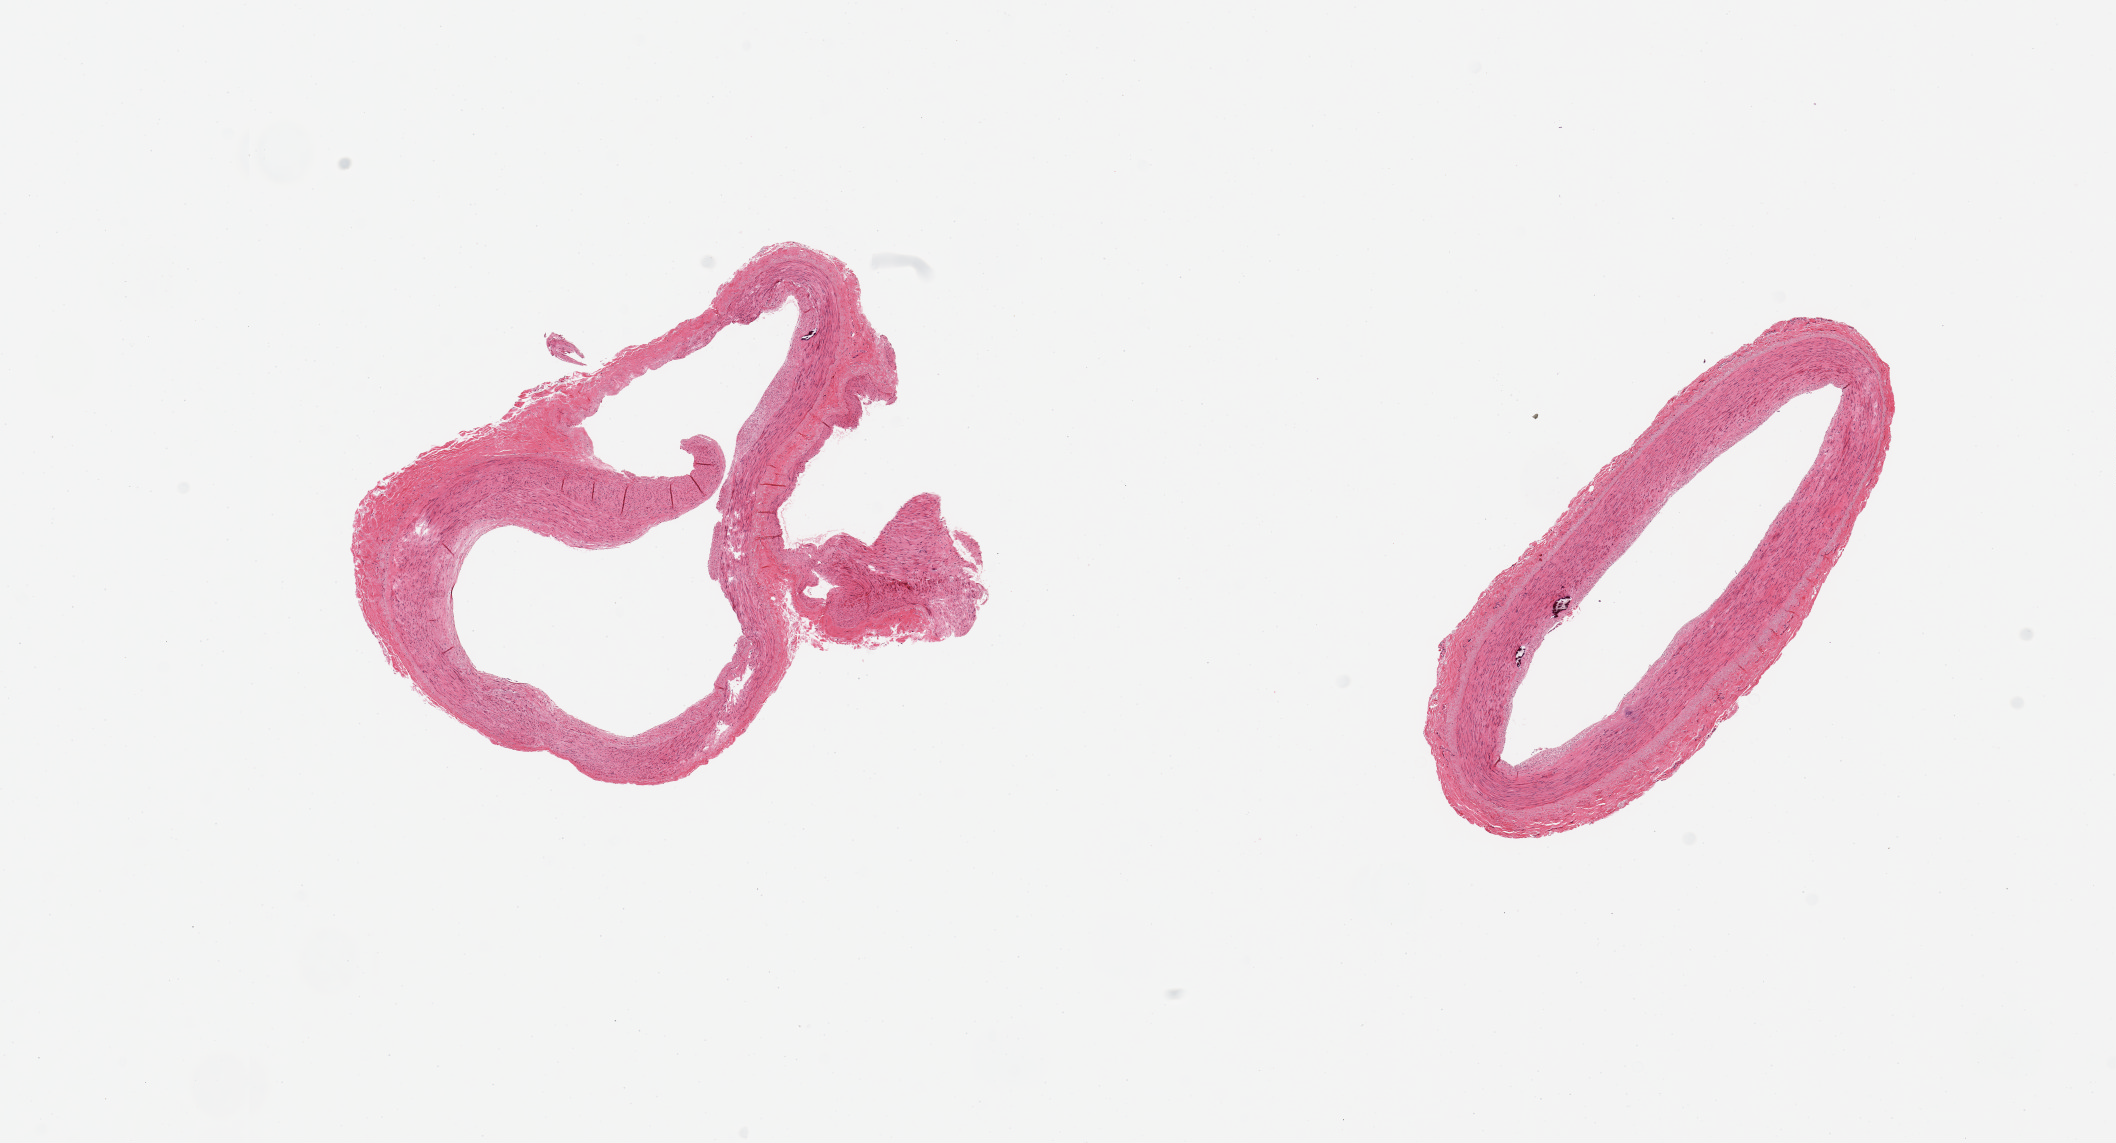
H&E whole-slide image, brightfield — a low-resolution overview of the entire scanned area, about 16.7 x 9.0 mm (slide scanned at 20x); PAXgene-fixed paraffin-embedded (PFPE) section; target tissue: tibial artery; donor tissue sample. Male donor.
Pathologist's review note for this sample: 2 pieces; fibrous plaque and small medial calcifications.